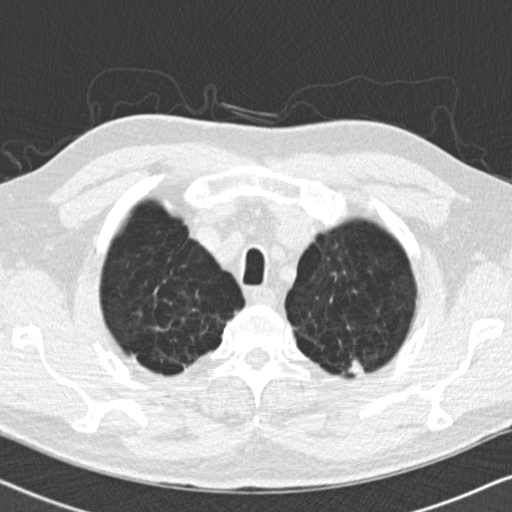
Low-dose screening chest CT, one axial slice; position 155 of 175 along the scan axis; reconstruction kernel B30f; 120 kVp; lung window (W 1500 / L -600 HU); 2 mm slice thickness; 512 × 512 image matrix, field of view 330 × 330 mm.
Annotated regions visible in this slice (outlined manually by an expert reader):
- lesion 1 (tumor, upper lobe of left lung): box from (x=349, y=359) to (x=364, y=375) px